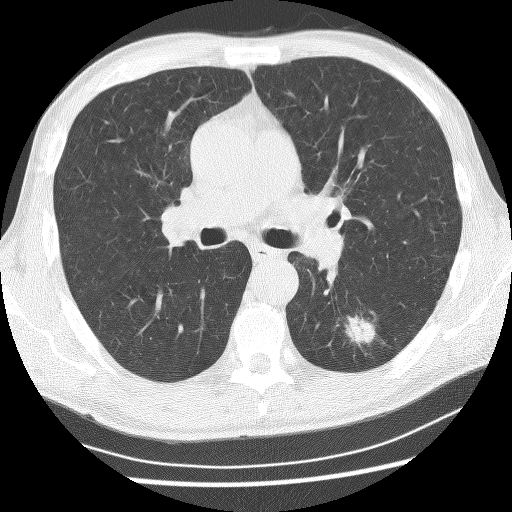
Low-dose screening chest CT, one axial slice. Slice 149 of 253 in the series (ordered by position). Reconstruction kernel BONE. 120 kVp. Lung window (W 1500 / L -600 HU). 2.5 mm slice thickness. 512 × 512 image matrix, field of view 340 × 340 mm.
Structures marked on this image (expert manual segmentation):
- lesion 1 (tumor, lower lobe of left lung): bounding box <345,316,376,345> (left, top, right, bottom; pixels)